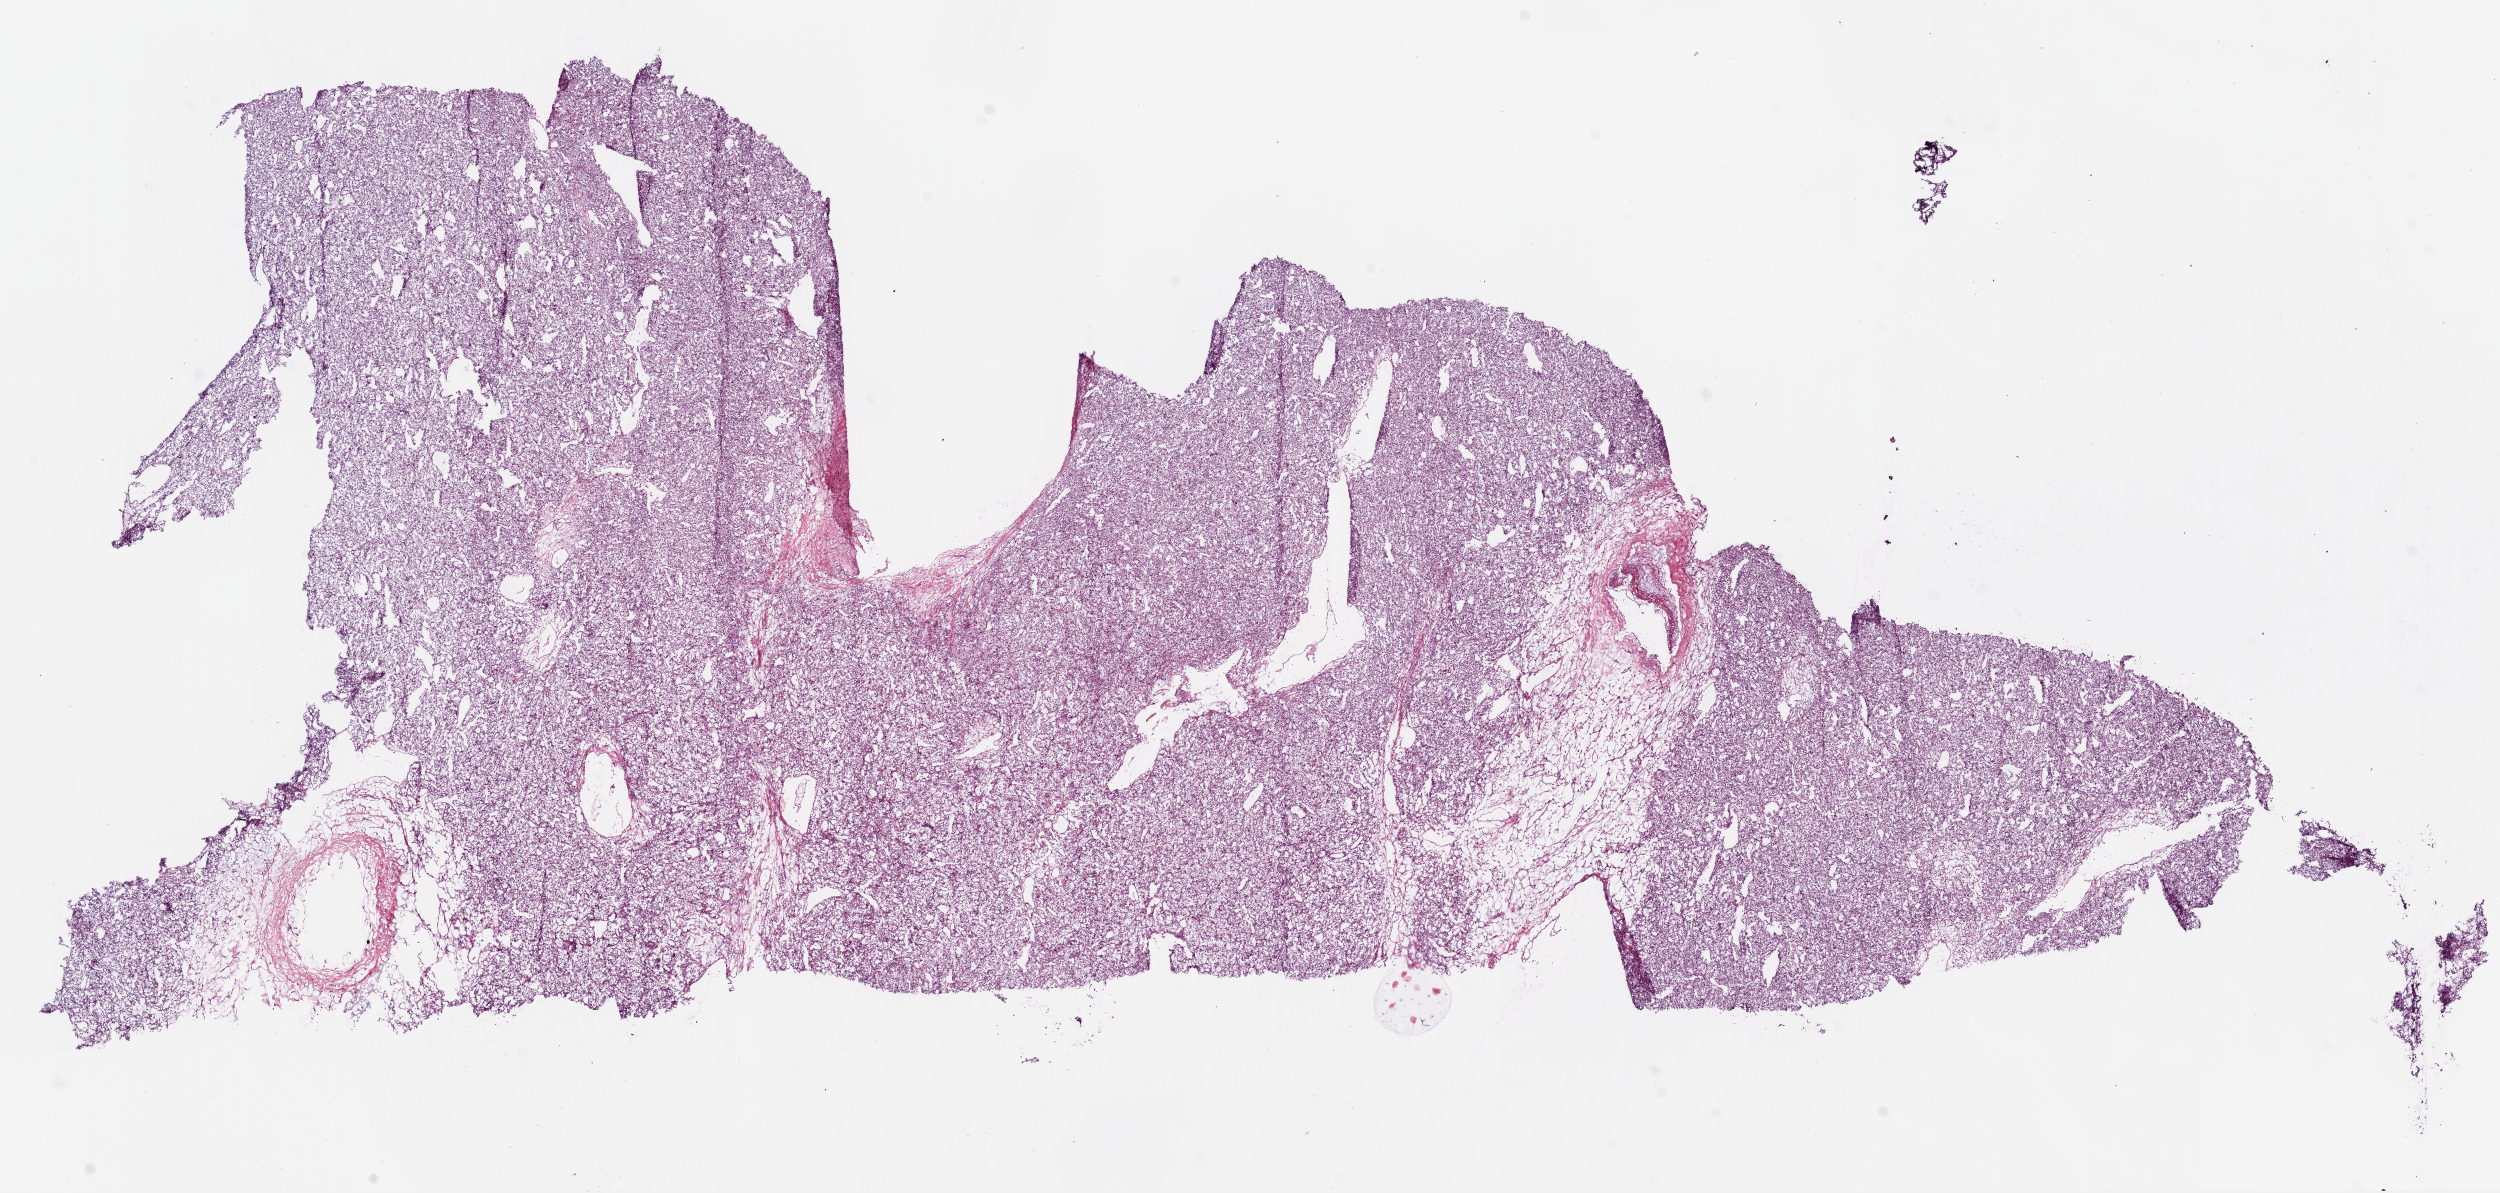
Digitized H&E tissue section (whole slide), a low-resolution overview of the entire scanned area, about 20.1 x 9.6 mm. Frozen section from the top of the tissue portion. Primary tumour sample from the kidney. Male patient; age at initial diagnosis 49 years. Histologic grade: G3 (poorly differentiated). Composition of this section per pathologist review: tumour cells 90%, tumour nuclei 90%, normal cells 0%, stromal cells 10%, necrosis 0%.
* AJCC pathologic stage: II (5th edition)
* pathologic diagnosis: Clear cell adenocarcinoma, NOS
* laterality: left
* TNM: T2 N0 M0